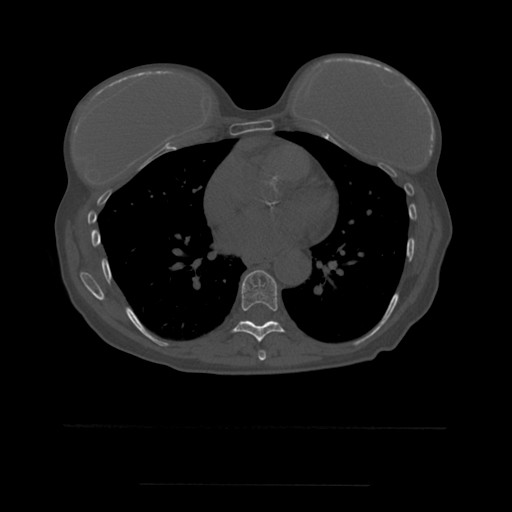
CT including the spine, one axial slice. Position 339 of 544 along the scan axis. Bone window (W 1800 / L 400 HU). 1.25 mm slice thickness. 512 × 512 image matrix, field of view 350 × 350 mm. Patient age 58 years. Case-level facts recorded for this patient, not image findings: primary cancer: lung.
Structures marked on this image (semi-automatically segmented with operator editing):
- T7 vertebra: bounding box [x1, y1, x2, y2] px = [258, 350, 267, 361]
- T8 vertebra: [233, 270, 285, 343]